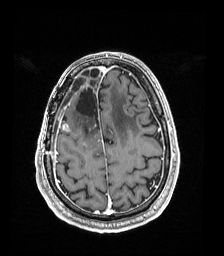
Brain MRI from a brain-tumour surgery series, one axial slice. Slice 49 of 192 in the series (ordered by position). T1-weighted post-contrast. 1 mm slice thickness. 224 × 256 image matrix, field of view 224 × 256 mm. From the clinical record (not read from this slice): histopathology: Astrocytoma; WHO grade: 4; IDH mutation: yes; tumour location: Right Frontal.
Annotated regions visible in this slice (outlined manually by an expert reader):
- previous resection cavity: box from (x=76, y=89) to (x=98, y=119) px